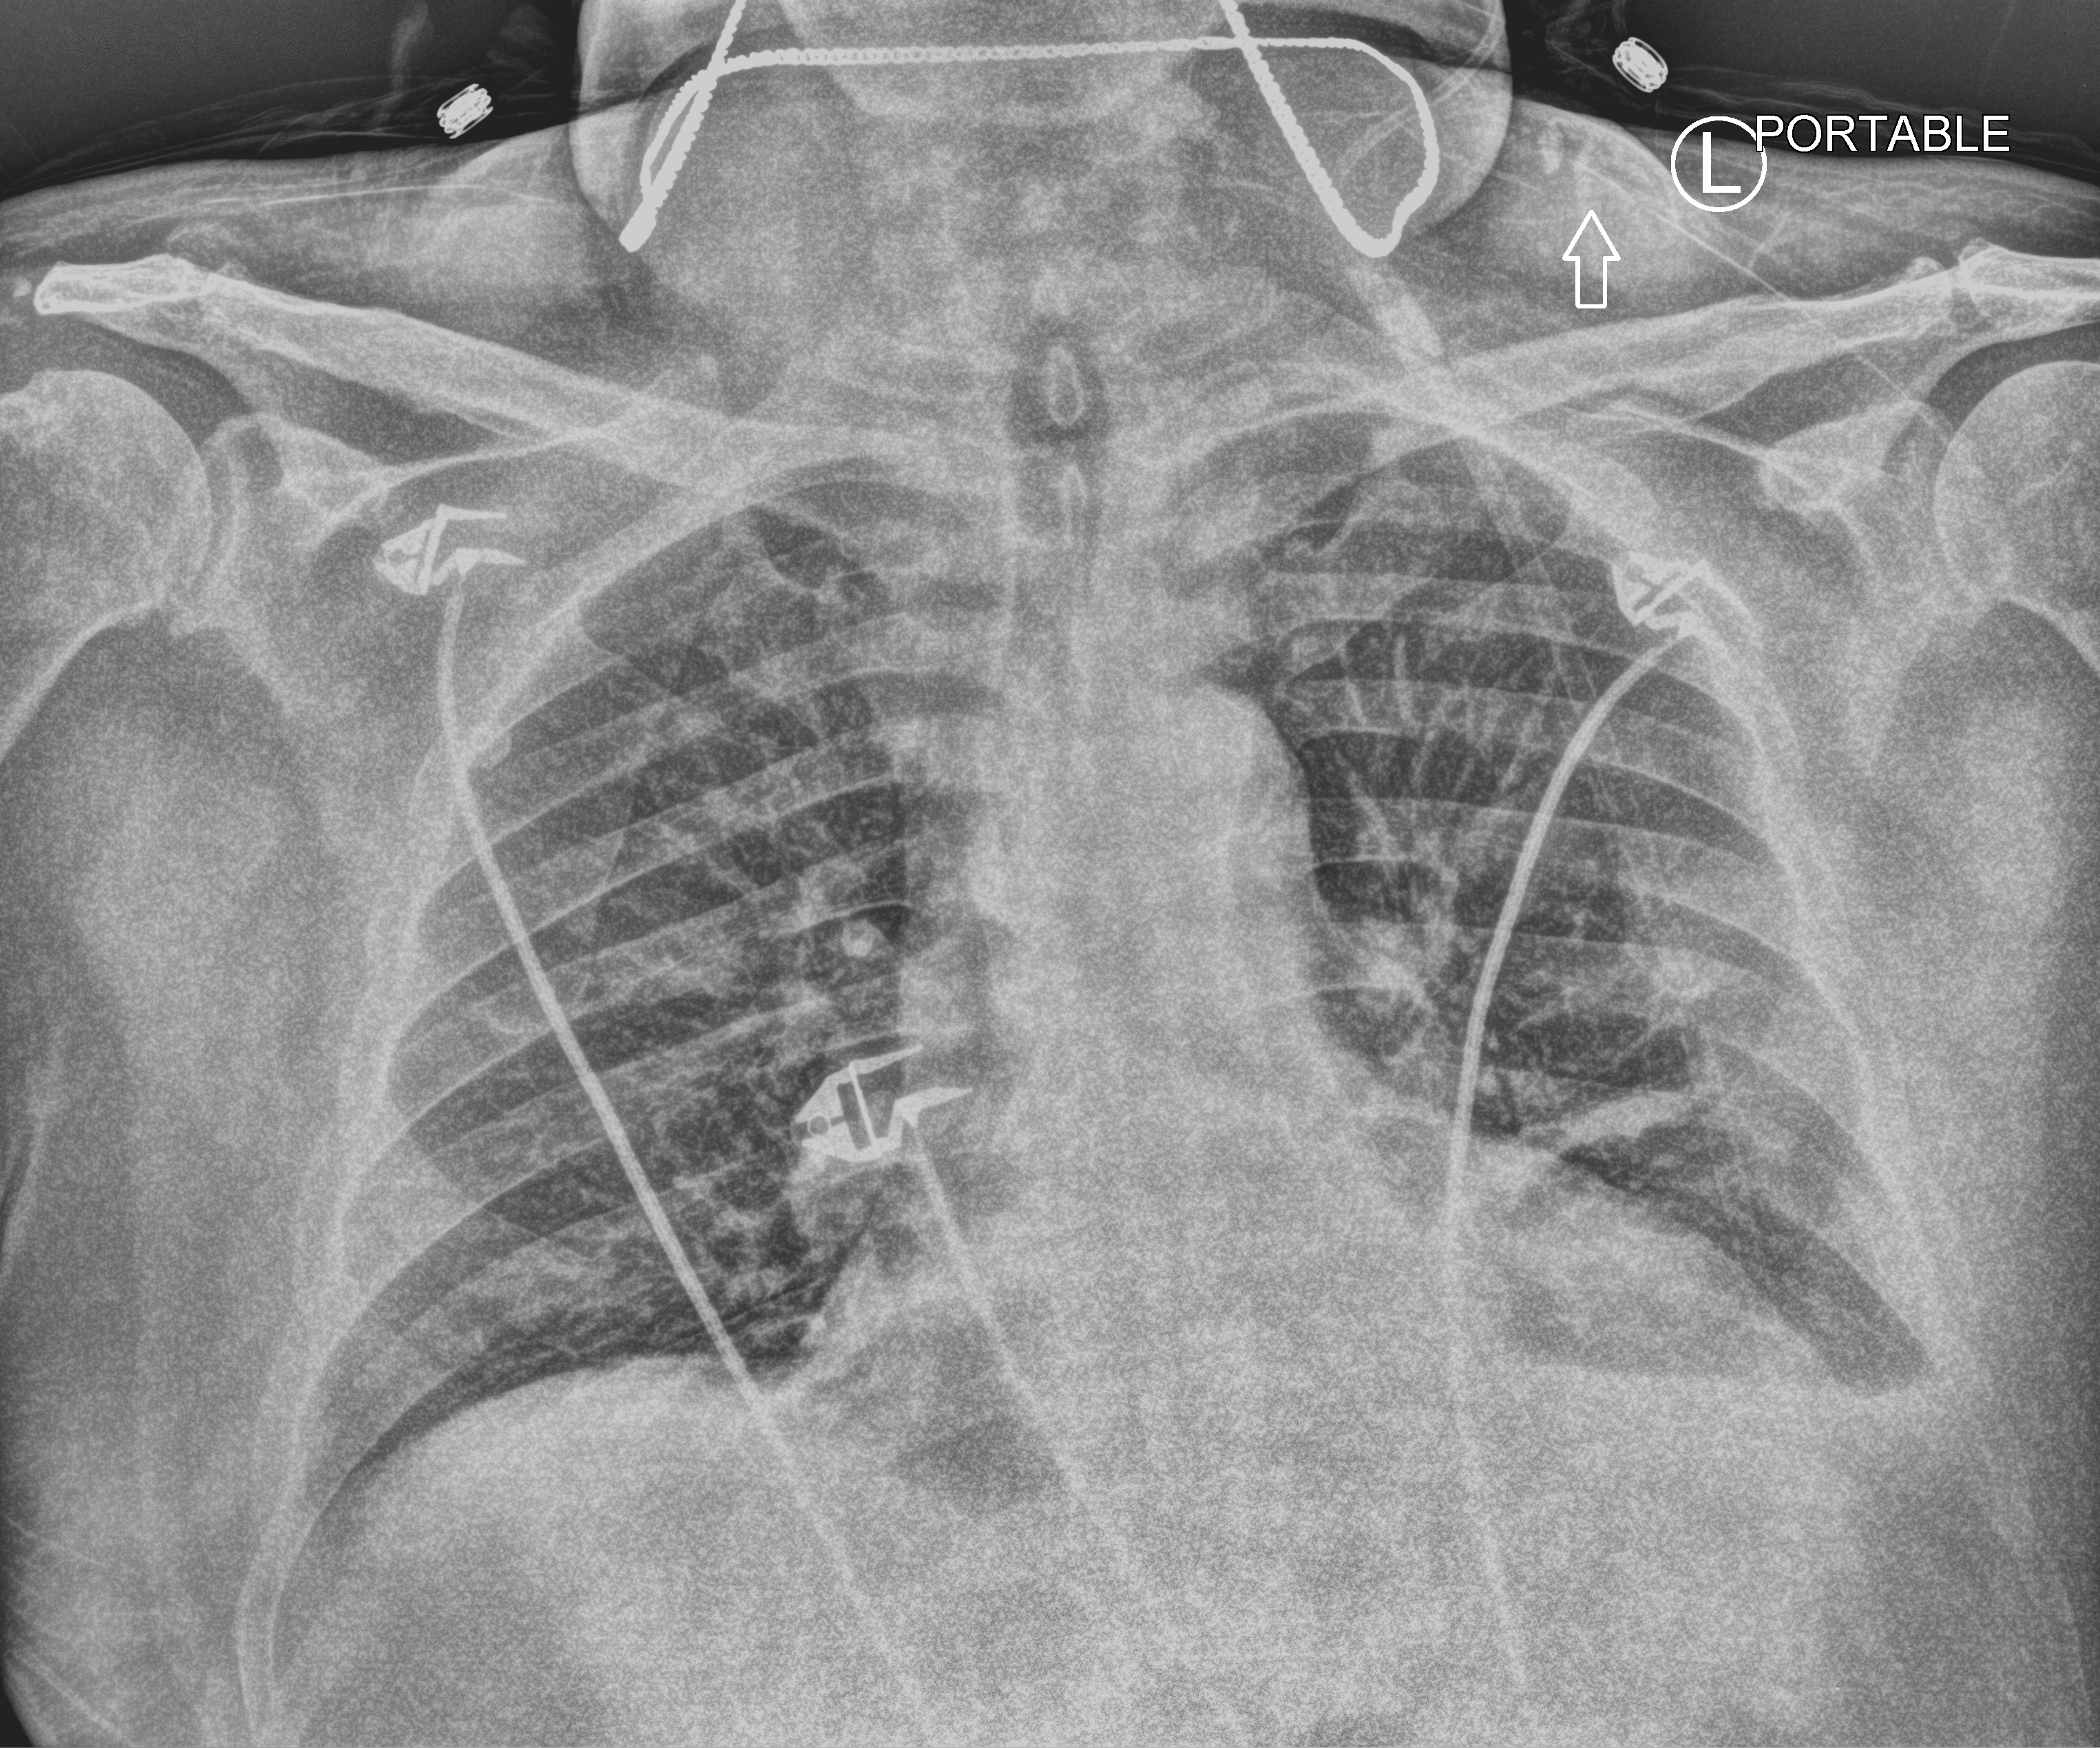
Portable chest radiograph; anteroposterior (AP) projection. Male patient hospitalised with COVID-19, age 60–74 years.
Hospital-stay facts (about this admission, not read from this image; timing relative to this image not recorded): admitted to intensive care during this hospital stay: no; mechanically ventilated during this hospital stay: no; diabetes (admission record): no.